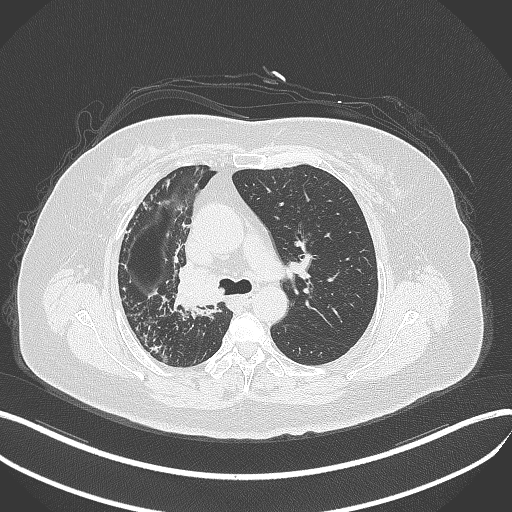
Chest CT, one axial slice; lung window (W 1500 / L -600 HU); 1 mm slice thickness; 512 × 512 image matrix, field of view 400 × 400 mm. Patient: female, 60 years. Case-level facts recorded for this patient, not image findings: clinical TNM (as recorded): T1c N0 M0.
Annotated regions visible in this slice (bounding box drawn by a radiologist):
- lung tumour (recorded histology: squamous cell carcinoma): bounding box (x1, y1, x2, y2) in pixels: (169, 261, 231, 313)